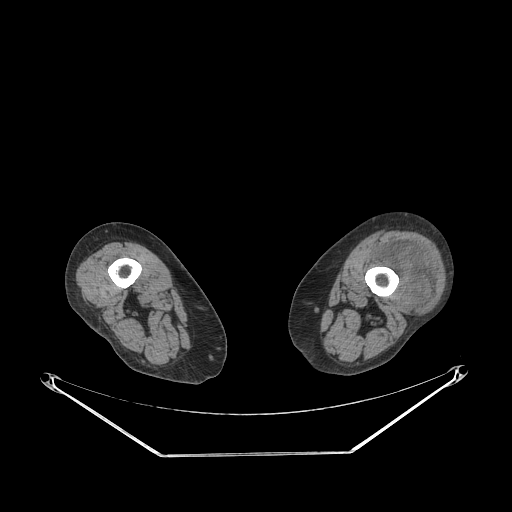
CT of an extremity soft-tissue mass (from a PET/CT study), one axial slice. Position 201 of 267 along the scan axis. 140 kVp. Soft-tissue window (W 400 / L 40 HU). 3.75 mm slice thickness. 512 × 512 image matrix. Female patient. Case-level facts recorded for this patient, not image findings: histological type: undifferentiated – high grade; grade: high; site of the primary tumour: left thigh.
Structures marked on this image (expert contour drawn on MRI and transferred to this co-registered scan by the dataset authors):
- gross tumour volume including surrounding oedema: bounding box <370,244,433,307> (left, top, right, bottom; pixels)